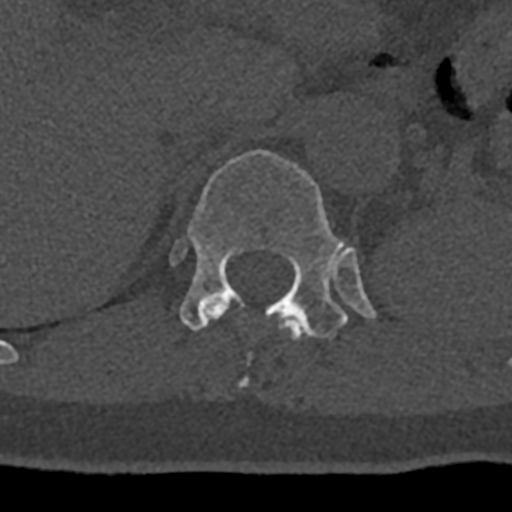
CT including the spine, one axial slice; position 507 of 797 along the scan axis; reconstruction kernel Br40s/3; bone window (W 1800 / L 400 HU); 0.5 mm slice thickness; 512 × 512 image matrix, field of view 160 × 160 mm. Male patient, age 74 years. From the clinical record (not read from this slice): primary cancer: renal.
Annotated regions visible in this slice (semi-automatic segmentation, software-assisted and operator-edited):
- T11 vertebra: bounding box [x1, y1, x2, y2] px = [206, 302, 304, 387]
- T12 vertebra: [171, 149, 376, 339]